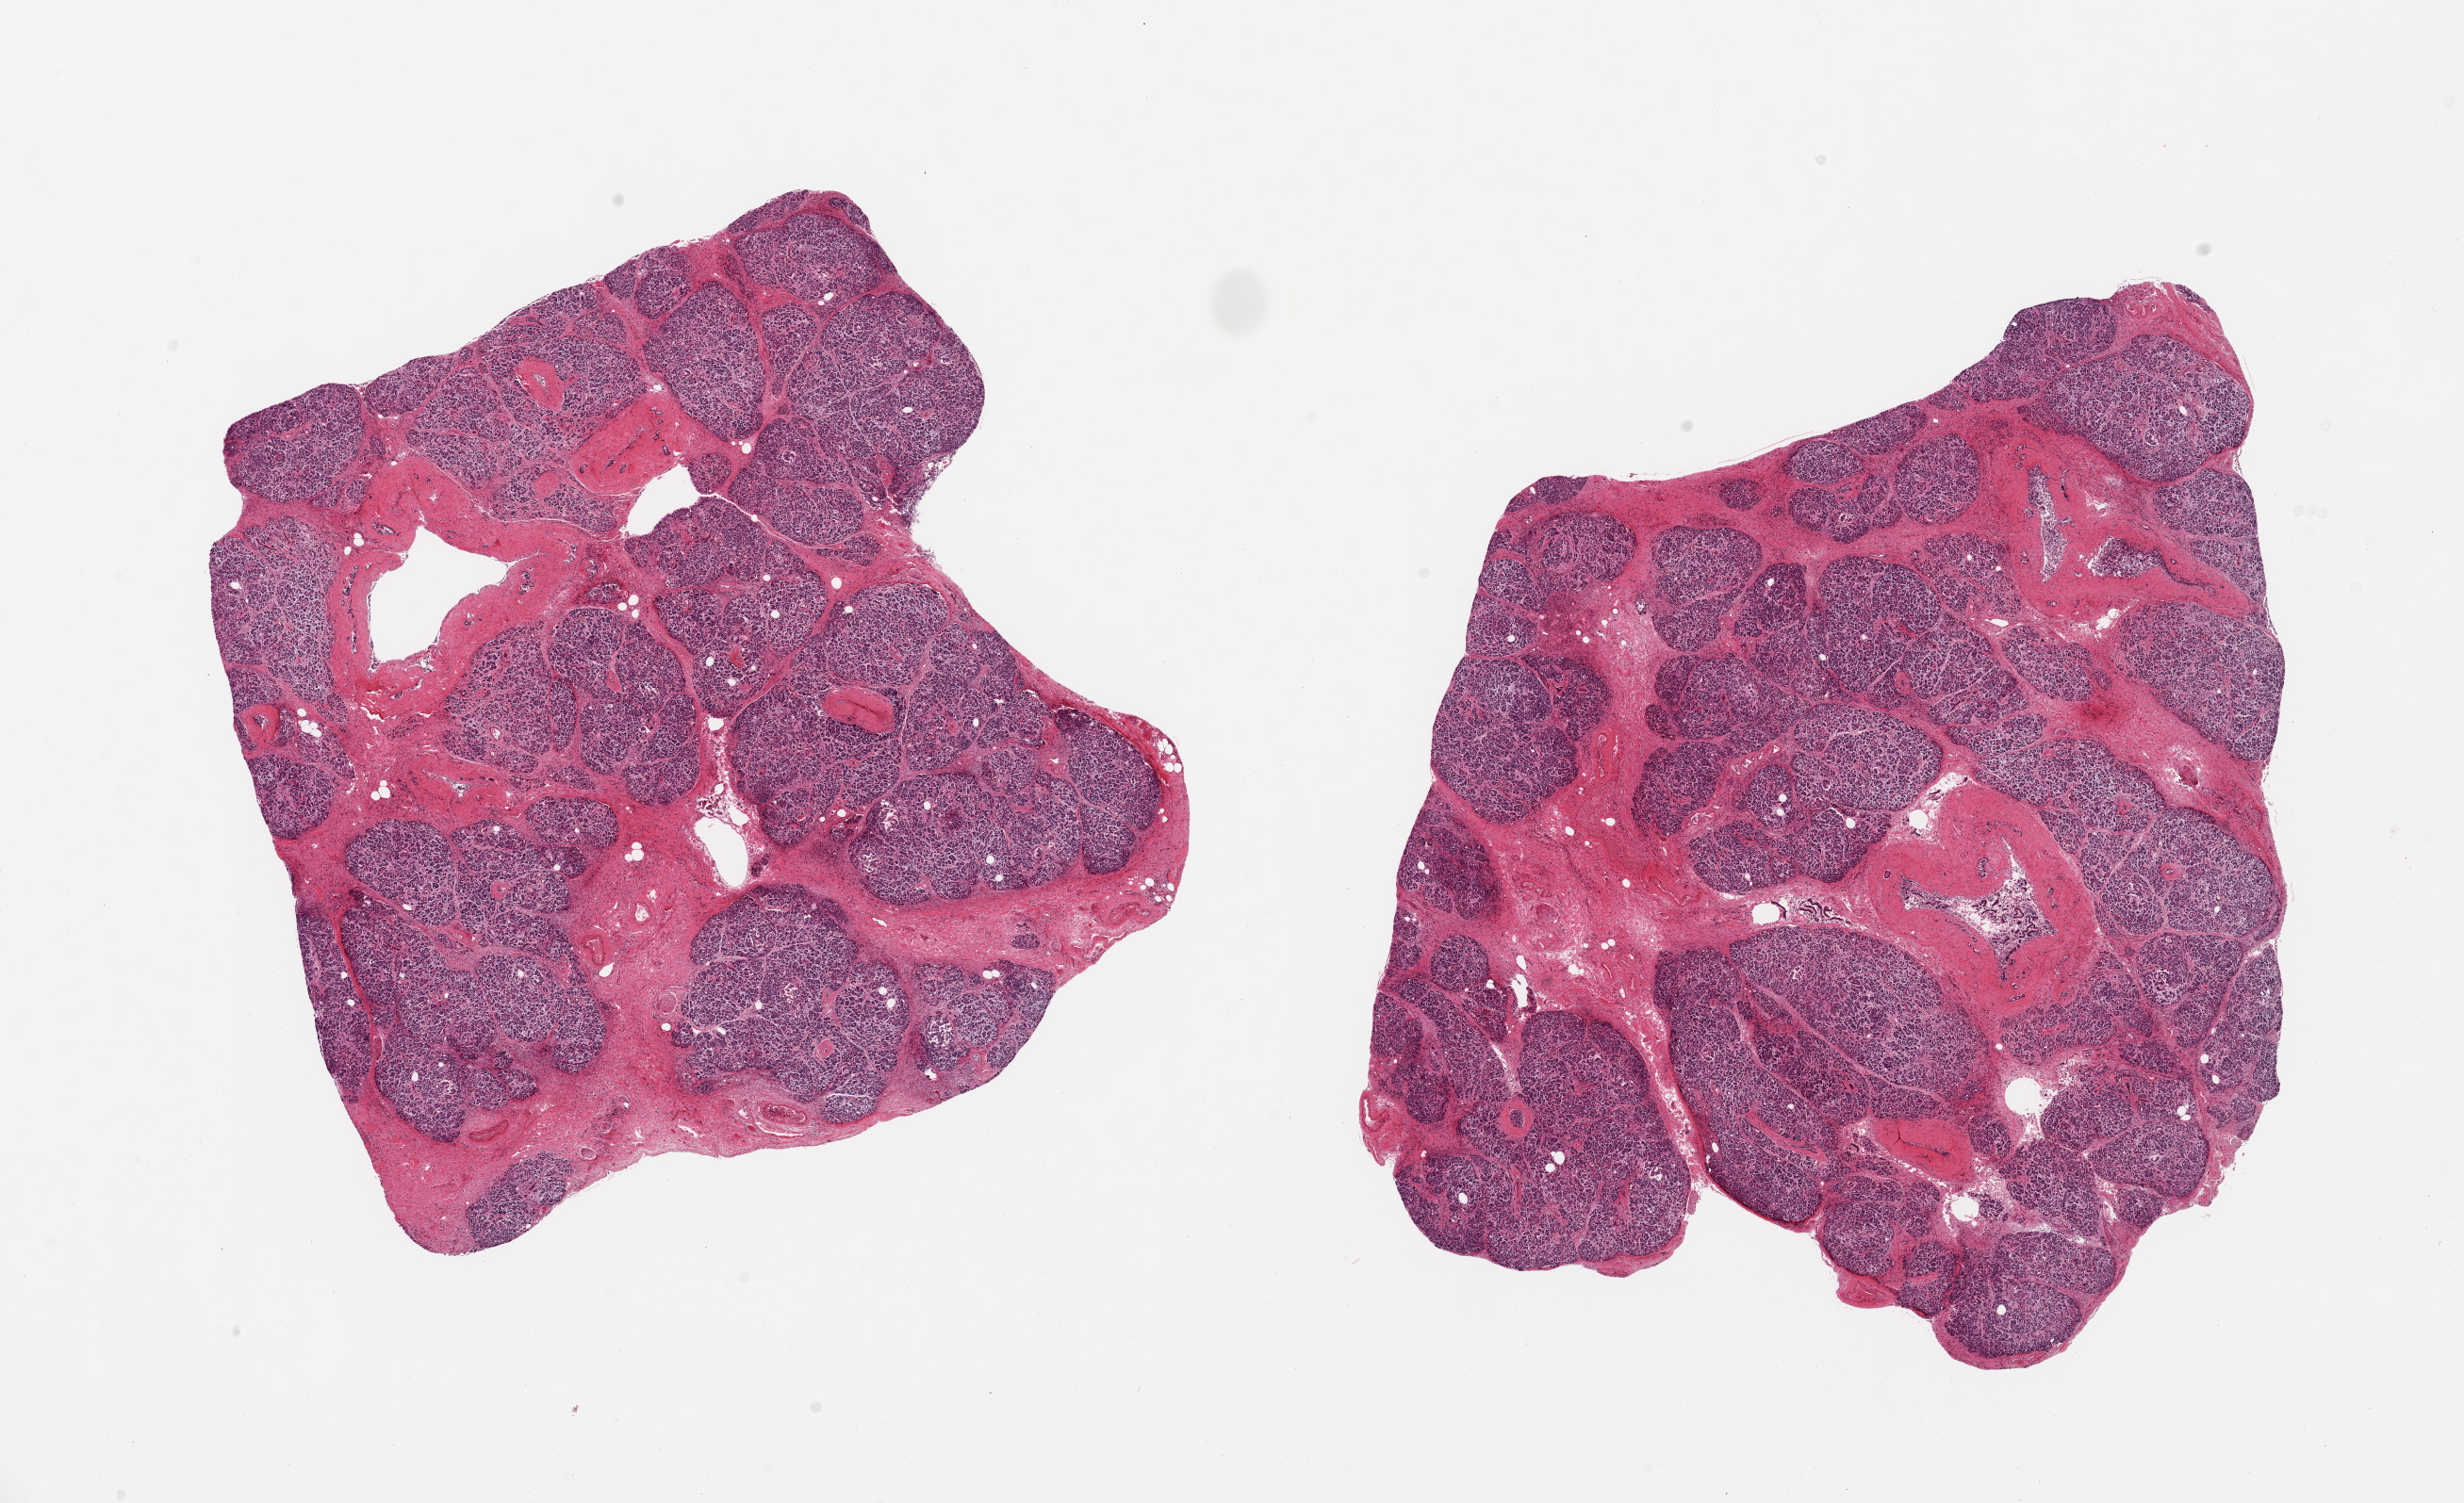
Digitized haematoxylin and eosin-stained section — whole scanned area (about 20.7 x 12.6 mm) shown as a low-resolution overview; PAXgene-fixed paraffin-embedded (PFPE) section; section of pancreas (target tissue); tissue donor sample. Donor sex: female.
• pathologist's review note for this sample: 2 pieces; moderate degree of nodular and diffuse fibrosis; contains several large ducts